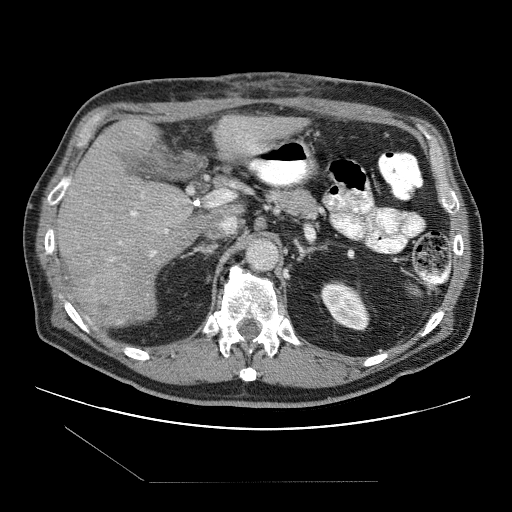
Contrast-enhanced abdominal CT (liver protocol), one axial slice. Slice 54 of 109 in the series (ordered by position). Reconstruction kernel STANDARD. One of 2 acquisitions stored at this slice position. Soft-tissue window (W 400 / L 40 HU). 2.5 mm slice thickness. 512 × 512 image matrix, field of view 400 × 400 mm. From the clinical record (not read from this slice): diagnosis: hepatocellular carcinoma (patient treated with transarterial chemoembolisation; whether this scan precedes or follows treatment is not stated here); TNM stage (as recorded): Stage-IIIB.
Outlined on this slice (semi-automatic segmentation, software-assisted and operator-edited):
- liver parenchyma outside the tumour (the mass and vessels are separate outlines, so this box may not span the whole liver): bounding box (x1, y1, x2, y2) in pixels: (54, 116, 306, 326)
- mass: (73, 265, 124, 327)
- liver vessels: (61, 142, 259, 261)